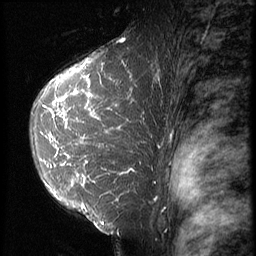
Breast MRI (dynamic contrast-enhanced), one sagittal slice; slice 42 of 64 in the series (ordered by position); 3 images stored at this slice position (order not interpretable as contrast timing); 1.5 T; TE 4.2 ms, TR 9 ms; 2.5 mm slice thickness; 256 × 256 image matrix, field of view 180 × 180 mm. Female patient, age 39 years. Case-level facts recorded for this patient, not image findings: setting: breast cancer imaged before/during neoadjuvant chemotherapy; receptor status: HER2-positive.
Outlined on this slice (semi-automatic segmentation, software-assisted and operator-edited):
- analysis volume of interest (the breast-tissue region the enhancement analysis was run in; not a lesion): bounding box <29,47,153,239> (left, top, right, bottom; pixels)
- tumour enhancement mask (voxels above the 140 % enhancement threshold inside the analysis volume of interest): <41,61,136,224>